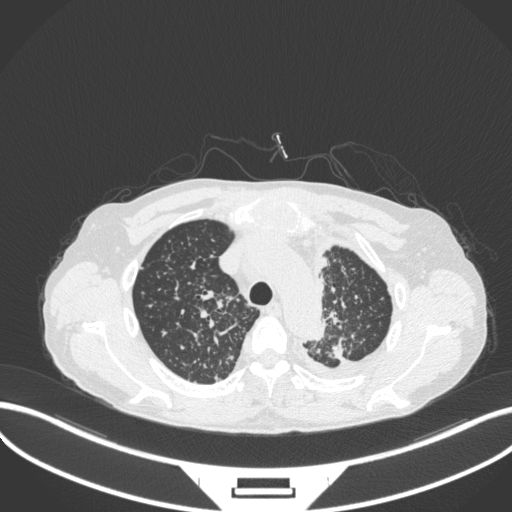
Chest CT, one axial slice. Position 276 of 319 along the scan axis. Reconstruction kernel B31f. 120 kVp. Lung window (W 1500 / L -600 HU). 1 mm slice thickness. 512 × 512 image matrix, field of view 400 × 400 mm. Male patient, age 58 years. Case-level facts recorded for this patient, not image findings: clinical TNM (as recorded): T1c N3 M1.
Outlined on this slice (bounding box drawn by a radiologist):
- lung tumour (recorded histology: adenocarcinoma): box from (x=328, y=335) to (x=348, y=358) px